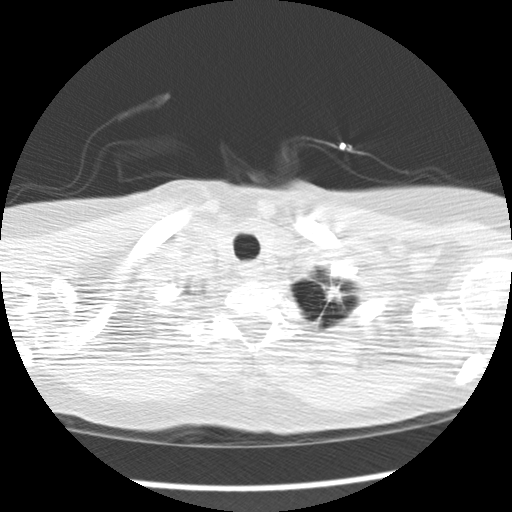
Axial slice from a low-dose chest CT screening exam; second screening round (one year after baseline); lung window (W 1500 / L -600 HU); standard (soft-tissue) reconstruction kernel (STANDARD); 120 kVp. Female participant, aged 69 years at enrolment. Former smoker at enrolment.
Expert reader's lesion annotation, bounding box <308,274,352,316> (left, top, right, bottom; pixels). The screening reader recorded 2 non-calcified nodules or masses ≥4 mm on this exam; which of them this box marks is not recorded. Participant outcome: lung cancer diagnosed 147 days after this screen — adenocarcinoma, NOS, left upper lobe, poorly differentiated (G3), stage IB (AJCC 6th edition), 80 mm at pathology.